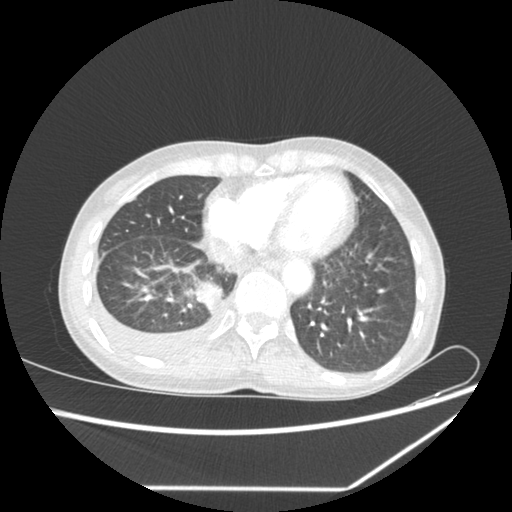
Chest CT, one axial slice; position 1 of 1 along the scan axis; reconstruction kernel SOFT; lung window (W 1500 / L -600 HU); 5 mm slice thickness; 512 × 512 image matrix. Patient: female, 59 years. From the clinical record (not read from this slice): clinical TNM (as recorded): T1c N1 M1.
Outlined on this slice (bounding box drawn by a radiologist):
- lung tumour (recorded histology: adenocarcinoma): box from (x=191, y=279) to (x=223, y=312) px